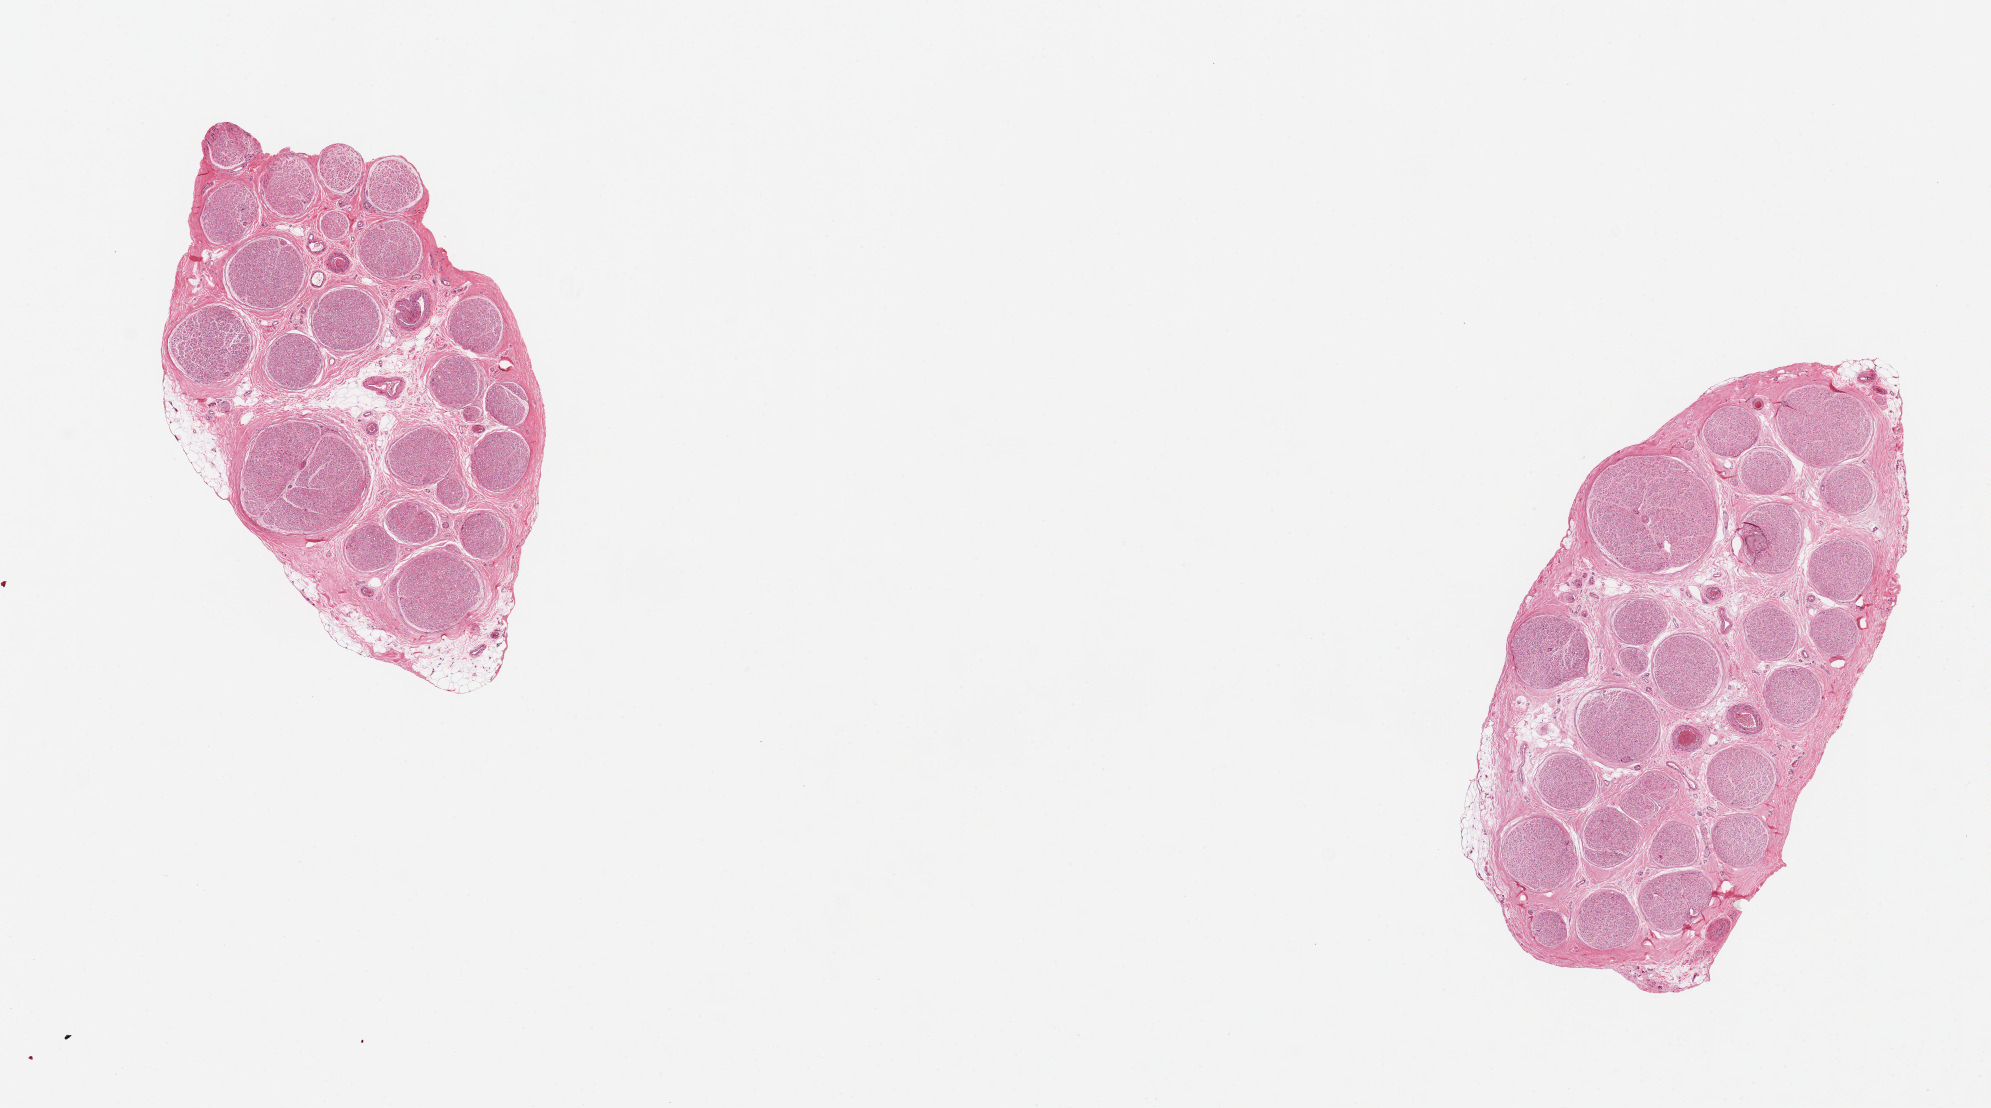
Whole-slide image, H&E stain, shown as a low-resolution overview of the whole scanned area (about 15.8 x 8.8 mm, acquisition: 20x scan). PAXgene-fixed, paraffin-embedded tissue. Sampled site (target tissue): tibial nerve. Donor tissue sample.
Pathologist's review note for this sample: 2 pieces ~3.5m d. Good clean specimens.